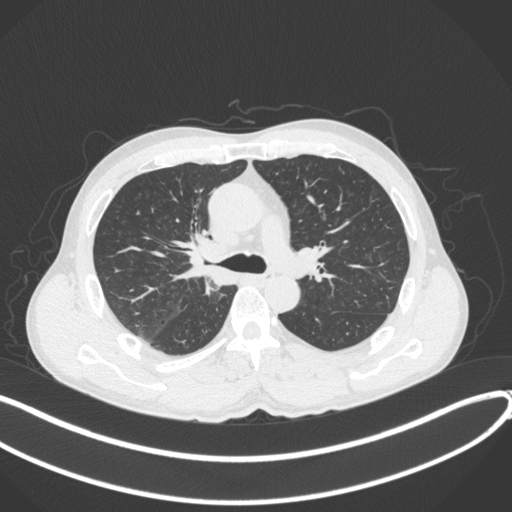
Chest CT, one axial slice; slice 250 of 409 in the series (ordered by position); reconstruction kernel B31f; lung window (W 1500 / L -600 HU); 512 × 512 image matrix, field of view 400 × 400 mm. Patient: male, 53 years. From the clinical record (not read from this slice): clinical TNM (as recorded): T1b N0 M0.
Outlined on this slice (bounding box drawn by a radiologist):
- lung tumour (recorded histology: squamous cell carcinoma): bounding box <178,237,234,289> (left, top, right, bottom; pixels)